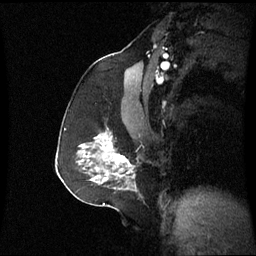
Breast MRI (dynamic contrast-enhanced), one sagittal slice; dynamic contrast-enhanced series, image 2 of 3 at this slice position (ordered by acquisition); 1.5 T; TE 4.2 ms, TR 8.9 ms; 2.4 mm slice thickness; 256 × 256 image matrix, field of view 230 × 230 mm. Patient: female, 59 years. Case-level facts recorded for this patient, not image findings: setting: breast cancer imaged before/during neoadjuvant chemotherapy; receptor status: triple-negative.
Outlined on this slice (semi-automatically segmented with operator editing):
- analysis volume of interest (the breast-tissue region the enhancement analysis was run in; not a lesion): bounding box (x1, y1, x2, y2) in pixels: (86, 132, 134, 183)
- tumour enhancement mask (voxels above the 70 % enhancement threshold inside the analysis volume of interest): (101, 143, 130, 166)